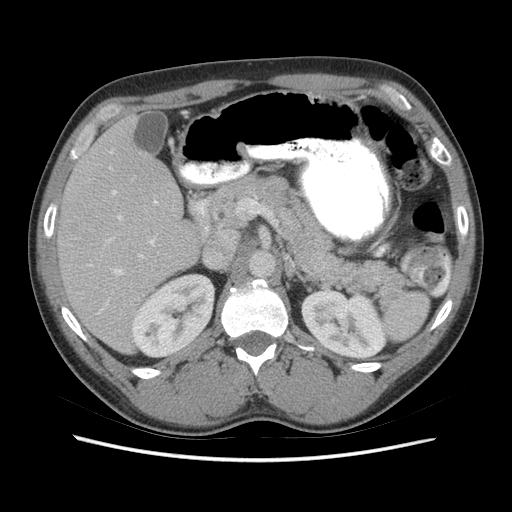
Contrast-enhanced abdominal CT (liver protocol), one axial slice; slice 32 of 73 in the series (ordered by position); reconstruction kernel STANDARD; 140 kVp; soft-tissue window (W 400 / L 40 HU); 2.5 mm slice thickness; 512 × 512 image matrix, field of view 360 × 360 mm. Case-level facts recorded for this patient, not image findings: diagnosis: hepatocellular carcinoma (patient treated with transarterial chemoembolisation; whether this scan precedes or follows treatment is not stated here); TNM stage (as recorded): Stage-IIIA; Child-Pugh class: A; tumour nodularity: multinodular.
Structures marked on this image (semi-automatically segmented with operator editing):
- liver parenchyma outside the tumour (the mass and vessels are separate outlines, so this box may not span the whole liver): bounding box [x1, y1, x2, y2] px = [56, 114, 210, 352]
- liver vessels: [97, 152, 208, 314]